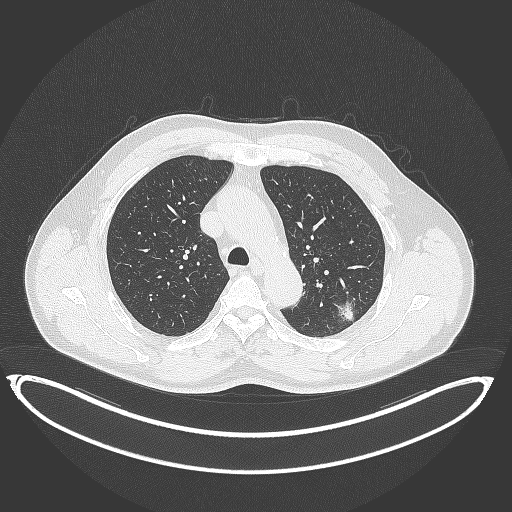
Chest CT, one axial slice; position 261 of 399 along the scan axis; reconstruction kernel B70f; 120 kVp; lung window (W 1500 / L -600 HU); 1 mm slice thickness; 512 × 512 image matrix, field of view 469 × 469 mm. Male patient, age 58 years. Case-level facts recorded for this patient, not image findings: clinical TNM (as recorded): T1c N0 M0.
Outlined on this slice (rectangle marked by the reading radiologist):
- lung tumour (recorded histology: adenocarcinoma): bounding box <333,296,362,328> (left, top, right, bottom; pixels)